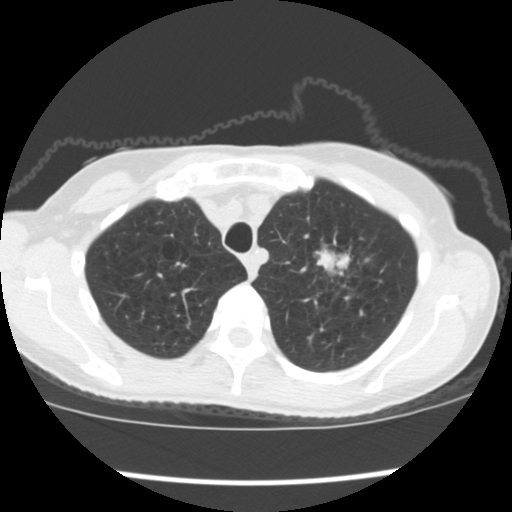
Chest CT (low-dose screening protocol), one axial image, first (baseline) screen, lung window (W 1500 / L -600 HU), standard (soft-tissue) reconstruction kernel (STANDARD), 120 kVp, slice 27 of 176 in the series. Female, age 67 years at enrolment. Former smoker at enrolment.
Lesion marked by an expert reader, box from (x=303, y=236) to (x=375, y=310) px. The exam's reader record, not a measurement of the box and not confirmed to be the same lesion: non-calcified nodule or mass ≥4 mm, left upper lobe, 34 × 32 mm, spiculated (stellate) margins, soft tissue attenuation, pre-existing on the prior screen: no. Participant outcome: lung cancer diagnosed 17 days after this screen — small cell carcinoma, NOS, left upper lobe, stage IIIA (AJCC 6th edition), 40 mm at pathology.